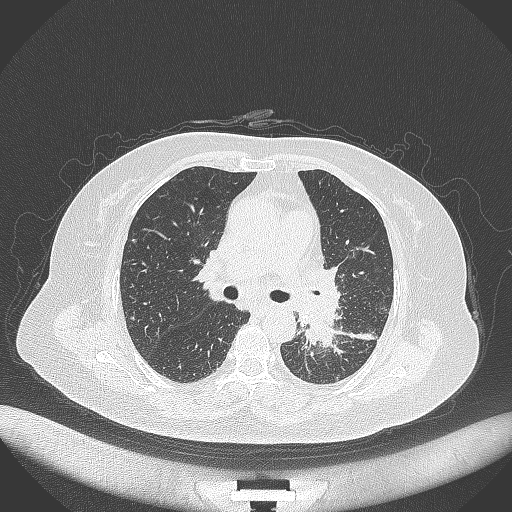
Chest CT, one axial slice; position 208 of 322 along the scan axis; lung window (W 1500 / L -600 HU); 1 mm slice thickness; 512 × 512 image matrix. Patient: female, 69 years. Case-level facts recorded for this patient, not image findings: clinical TNM (as recorded): T2b N3 M1.
Structures marked on this image (rectangle marked by the reading radiologist):
- lung tumour (recorded histology: adenocarcinoma): box from (x=301, y=312) to (x=337, y=353) px